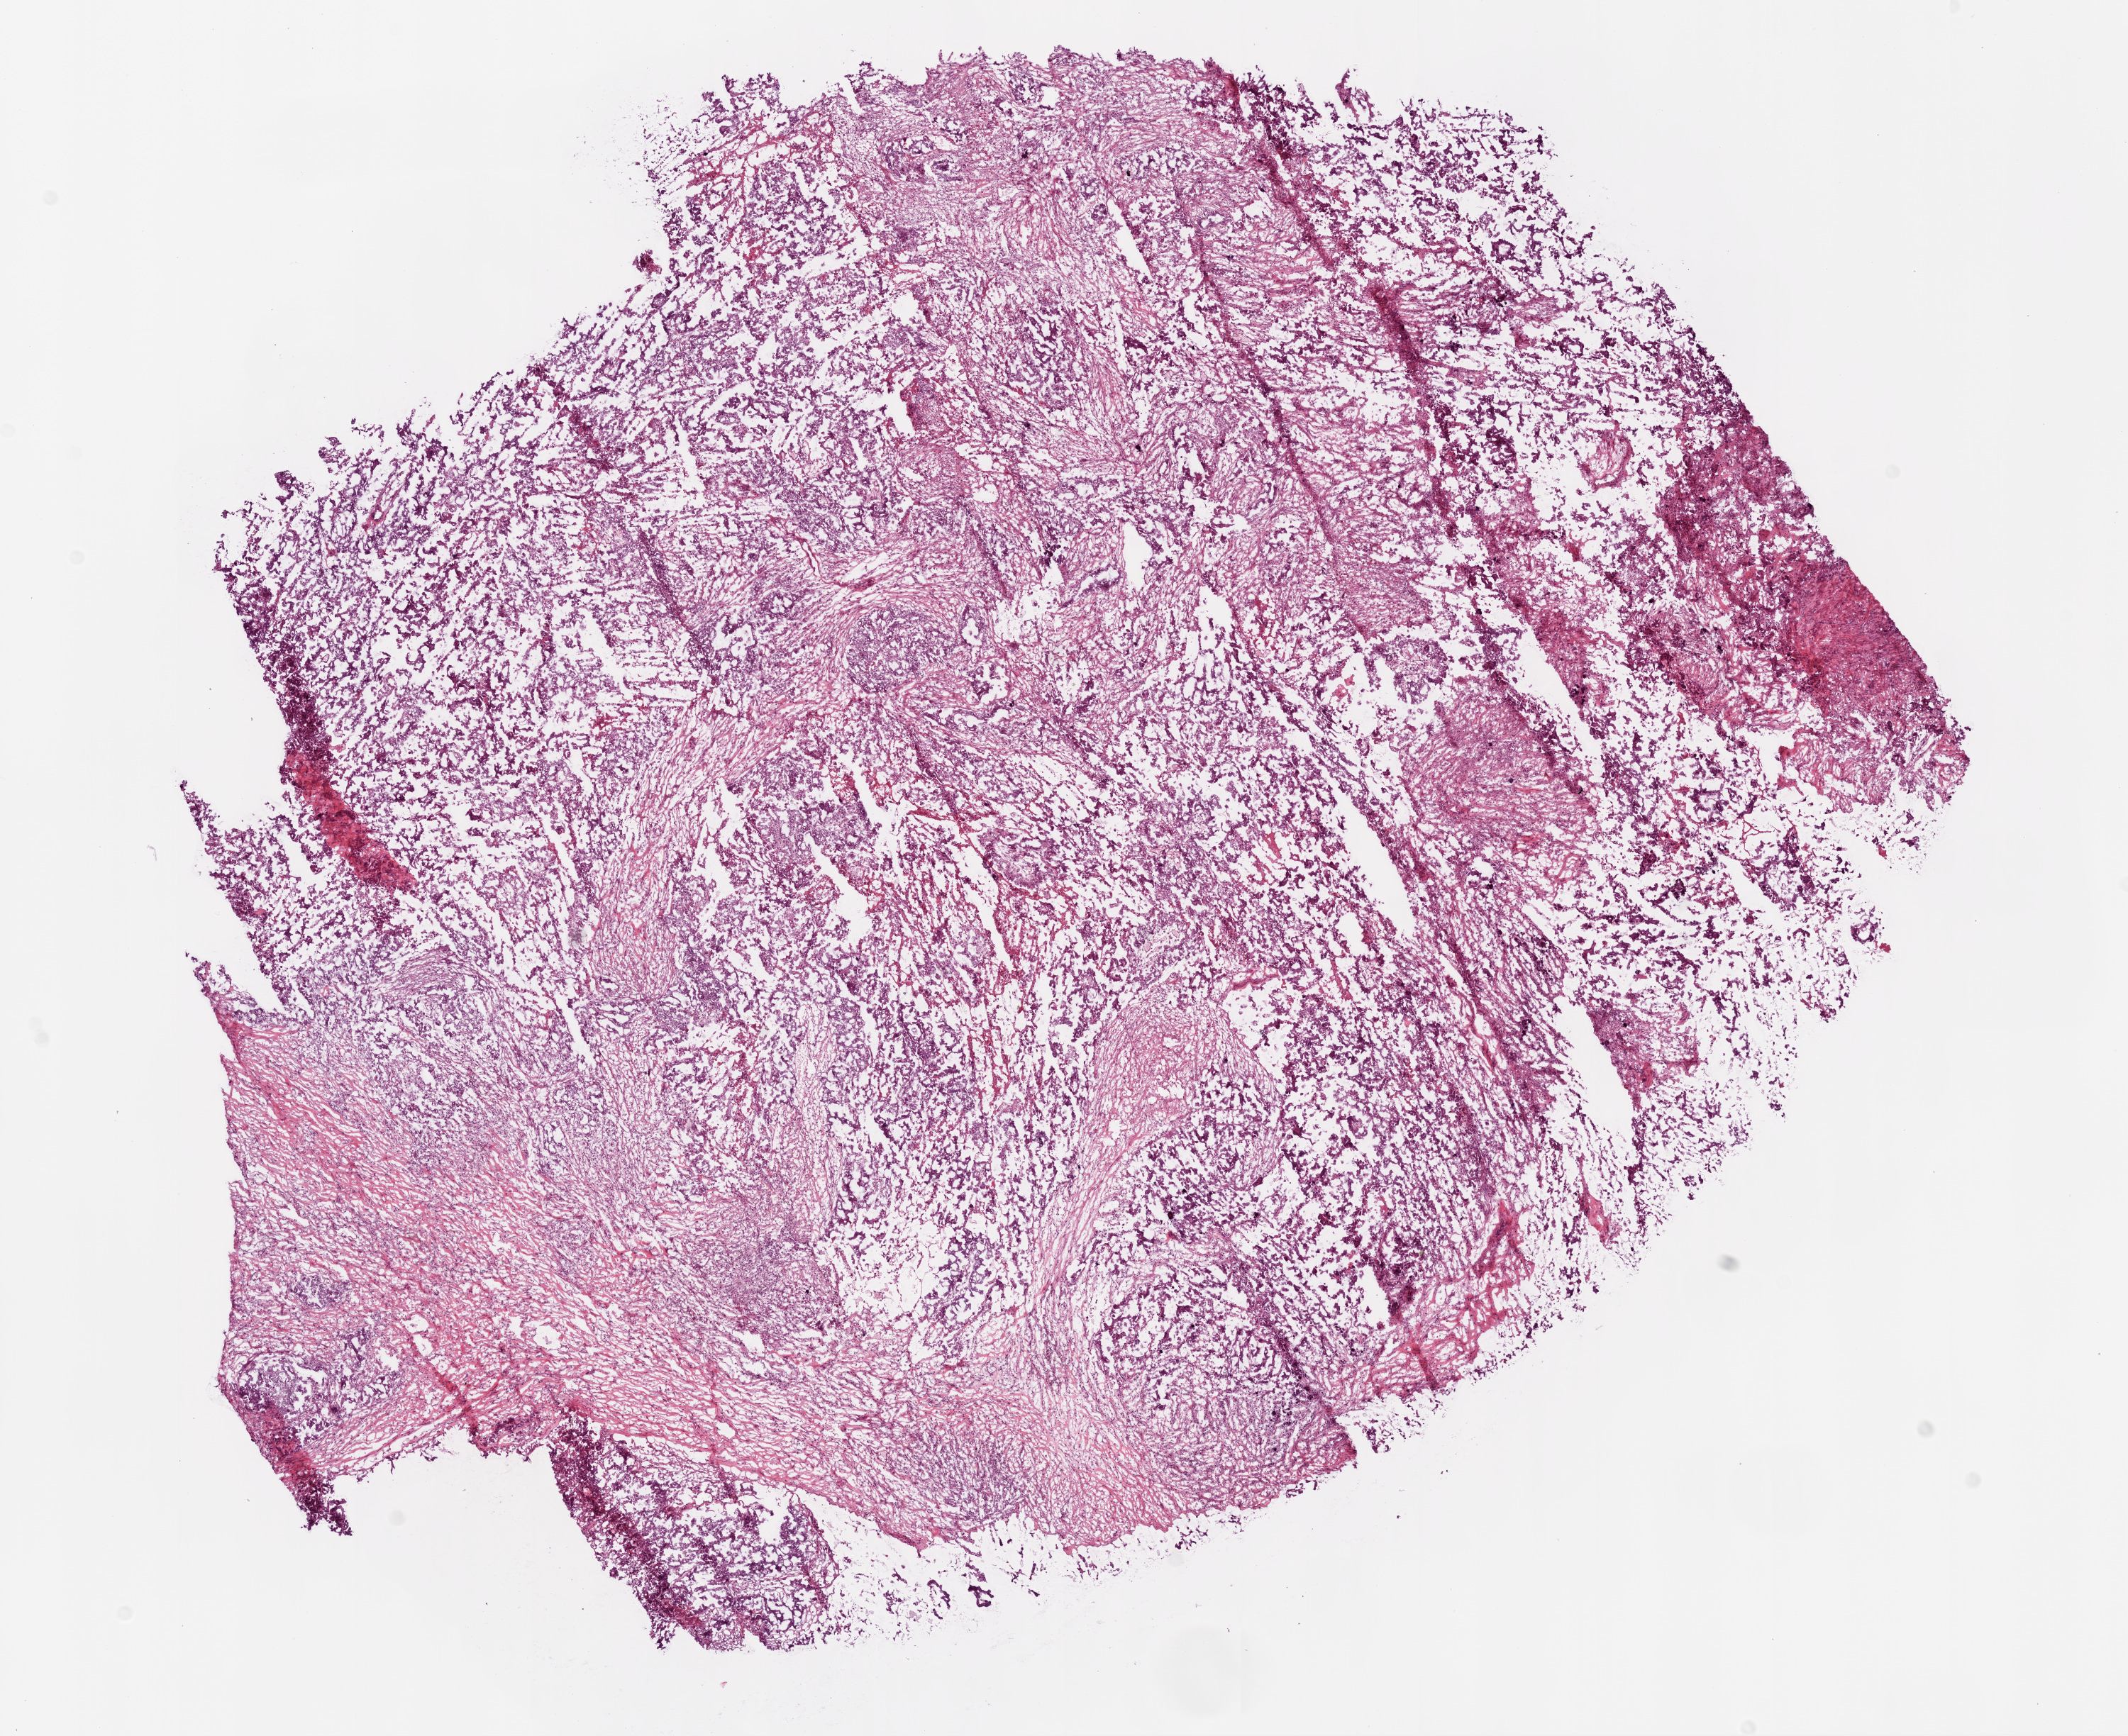
Digitized Hematoxylin and eosin (H&E) stained tissue section (whole slide) — shown as a low-resolution overview of the whole scanned area (about 12.0 x 9.8 mm). Frozen section from the bottom of the tissue portion. Ovary, primary tumour sample. Patient: female, age at initial diagnosis 75 years. Histologic grade: G3 (poorly differentiated). Pathologist review of this section (percent, as recorded): tumour cells 70%, tumour nuclei 85%, normal cells 0%, stromal cells 30%, necrosis 0%. Inflammatory infiltration, as recorded: lymphocyte infiltration 0%, monocyte infiltration 2%, neutrophil infiltration 0%.
FIGO stage: IIIC. Laterality: bilateral. Diagnosis: Serous cystadenocarcinoma, NOS.